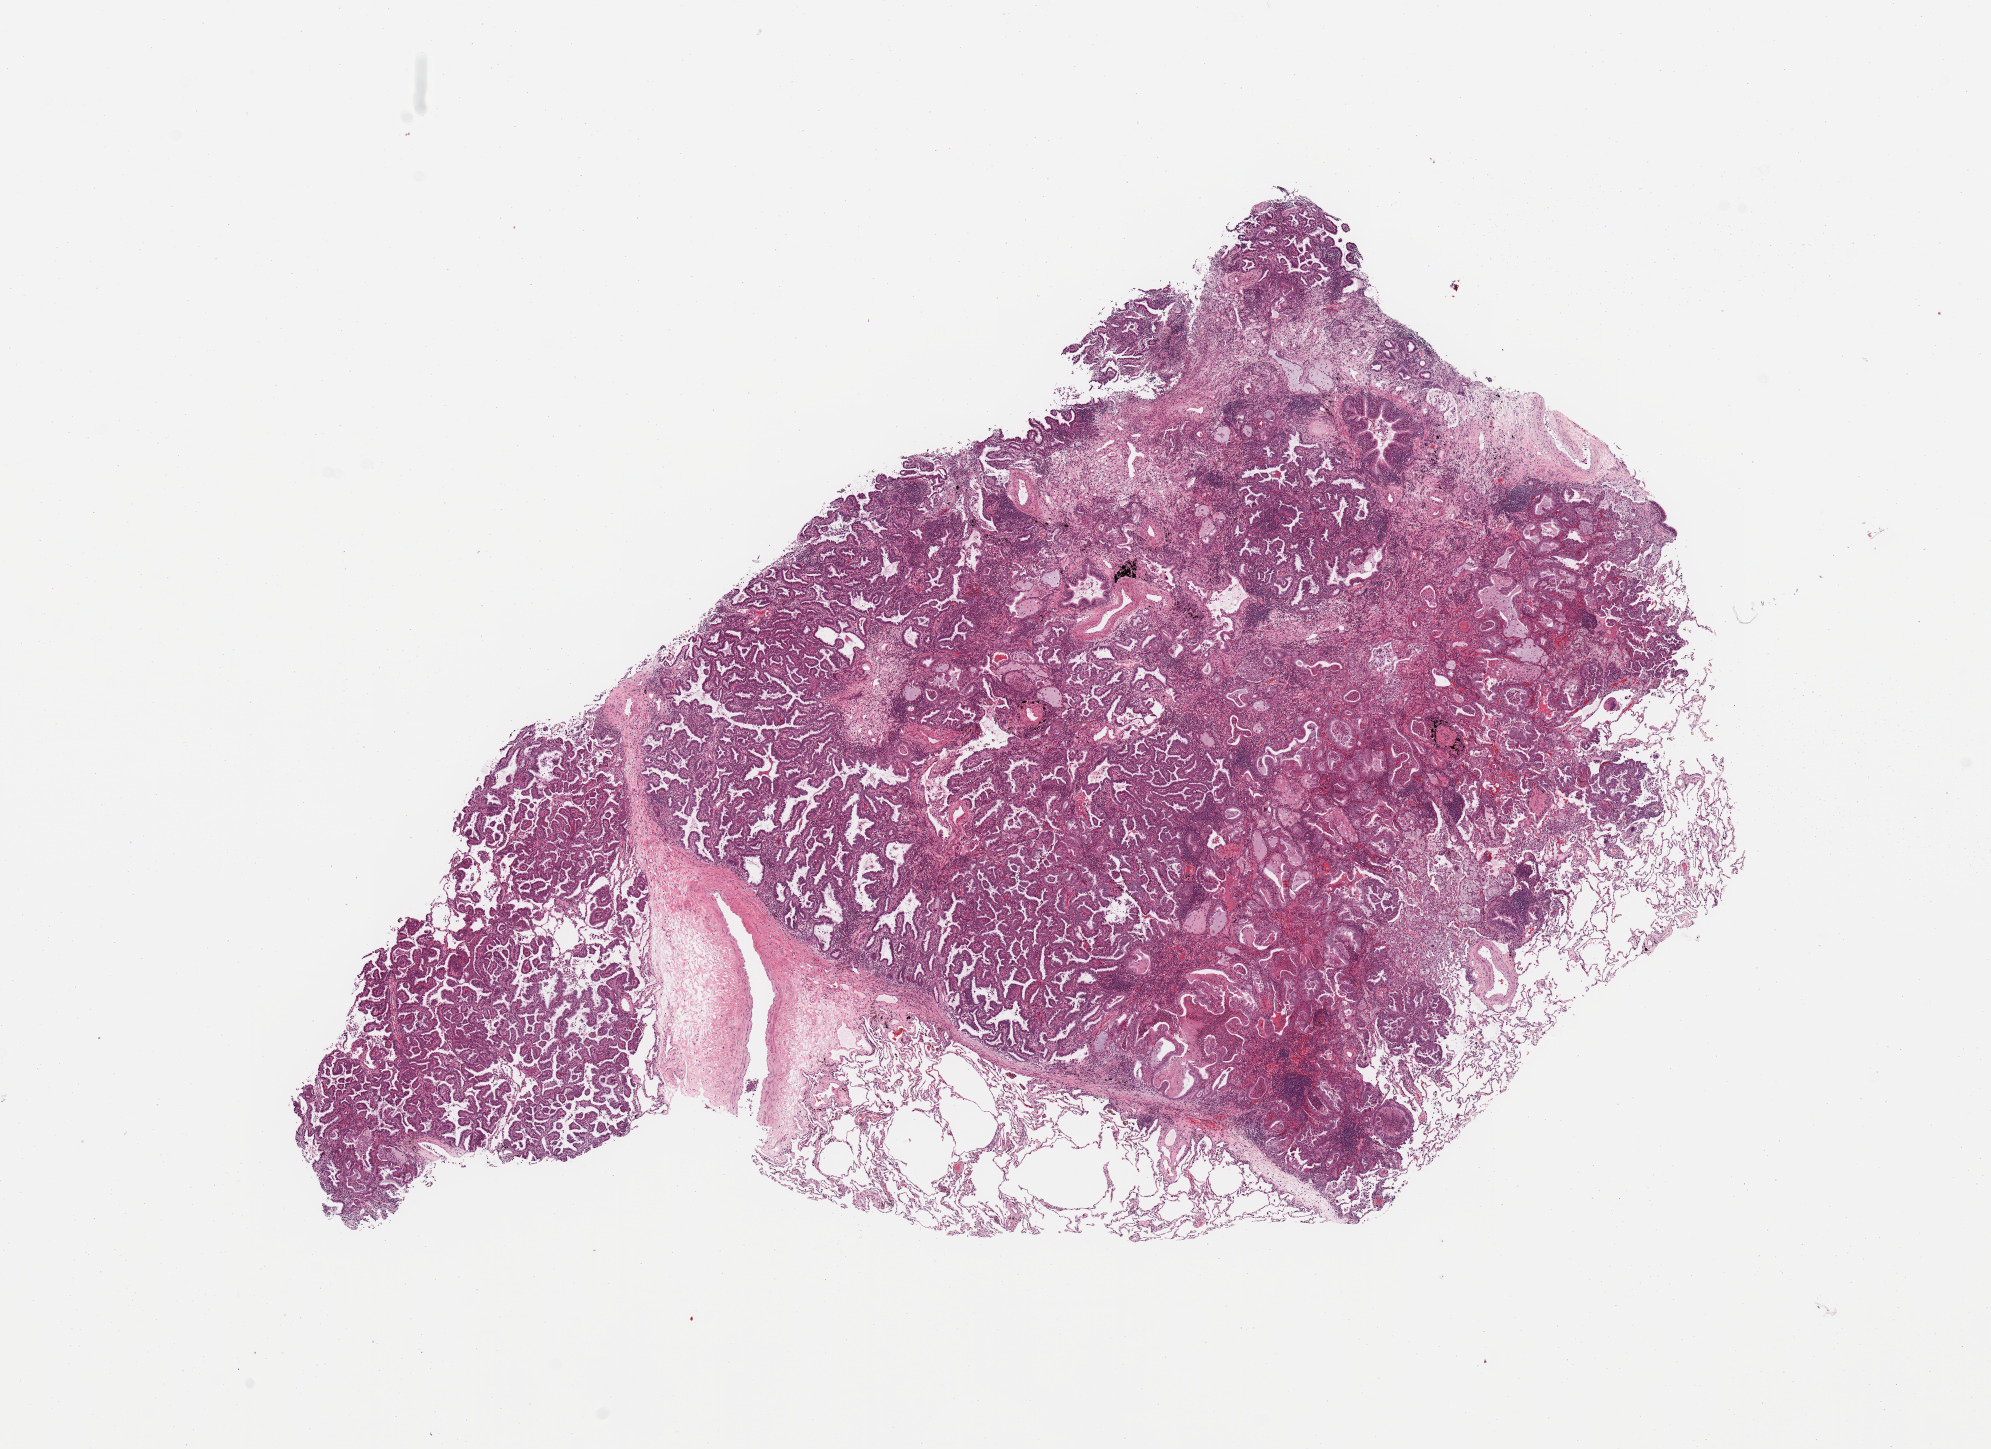
Digitized H&E-stained tissue section (whole slide), shown as a low-resolution overview of the whole scanned area (about 15.8 x 11.5 mm). Tumour tissue sample, lung. Patient: female, age 58 years. Histologic grade: G2 (moderately differentiated).
AJCC pathologic stage: IIA. Primary tumour site (as recorded): right lower lobe. Diagnosis: Adenocarcinoma, NOS.